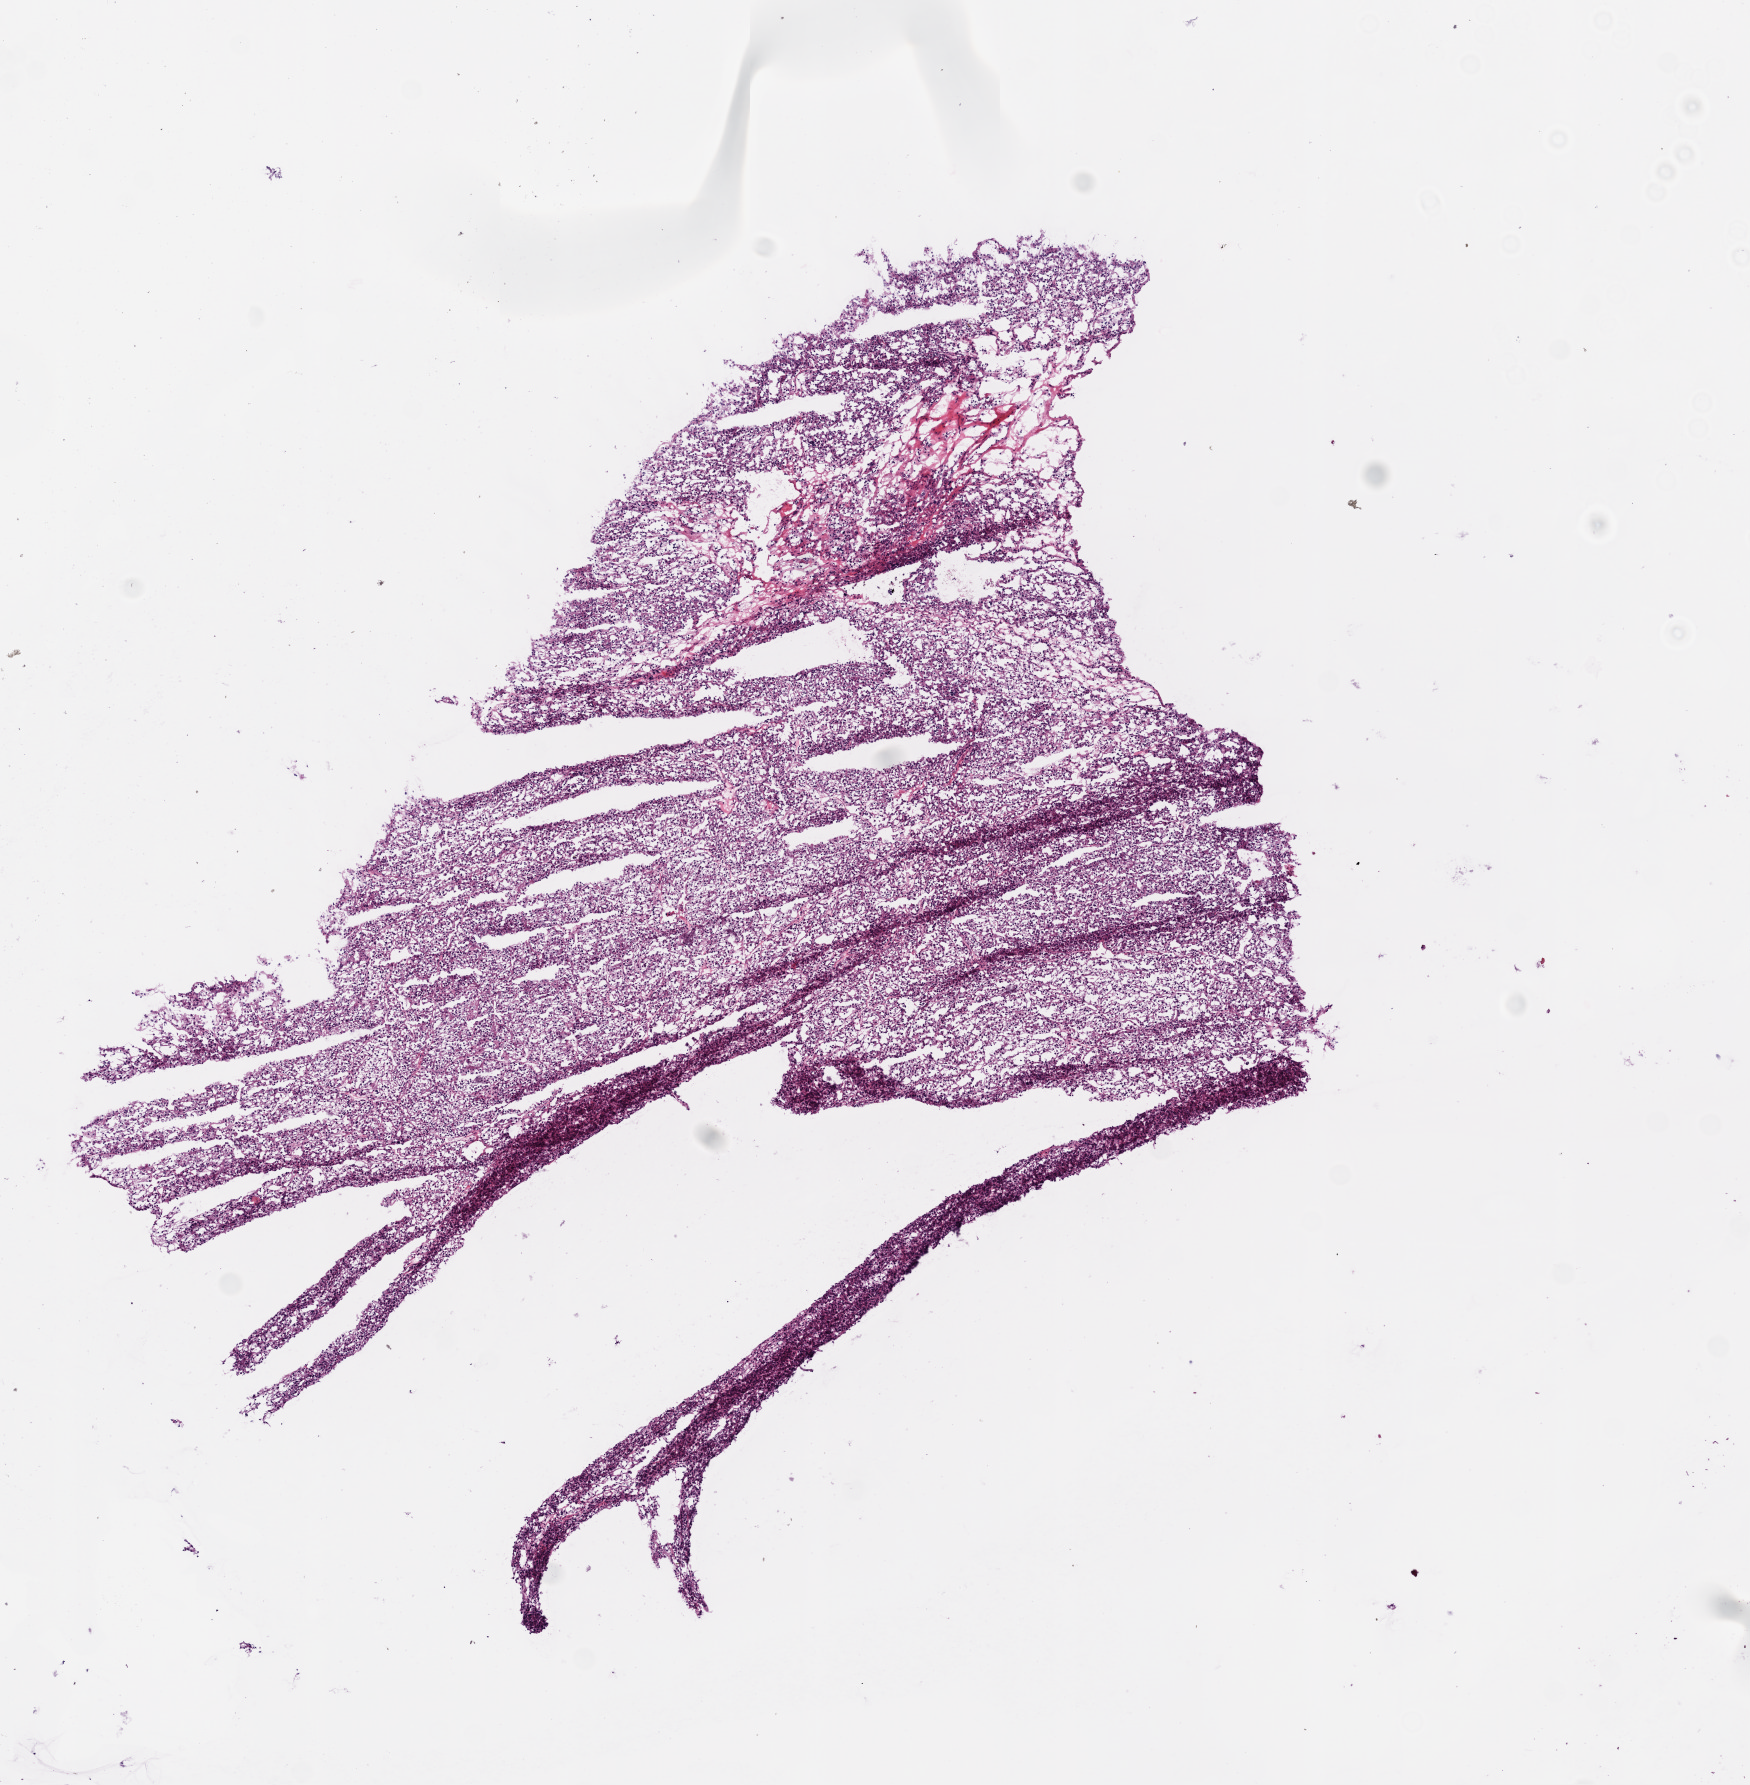
Digitized H&E-stained tissue section (whole slide), whole scanned area (about 7.0 x 7.2 mm, slide scanned at 20x) shown as a low-resolution overview. Frozen section. Kidney, primary tumour sample. Female, age 46 years at initial diagnosis. Histologic grade: G2 (moderately differentiated). Pathologist review of this section (percent, as recorded): tumour cells 93%, tumour nuclei 85%, normal cells 0%, stromal cells 7%, necrosis 0%.
* histologic diagnosis: Clear cell adenocarcinoma, NOS
* AJCC pathologic stage: I